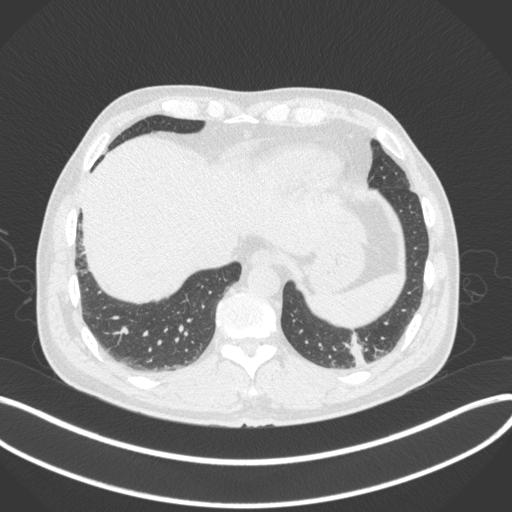
Chest CT, one axial slice. Position 53 of 313 along the scan axis. Reconstruction kernel B31f. 120 kVp. Lung window (W 1500 / L -600 HU). 1 mm slice thickness. 512 × 512 image matrix. Patient: male, 54 years. From the clinical record (not read from this slice): clinical TNM (as recorded): T1c N0 M1.
Annotated regions visible in this slice (rectangle marked by the reading radiologist):
- lung tumour (recorded histology: adenocarcinoma): bounding box [x1, y1, x2, y2] px = [344, 332, 373, 369]